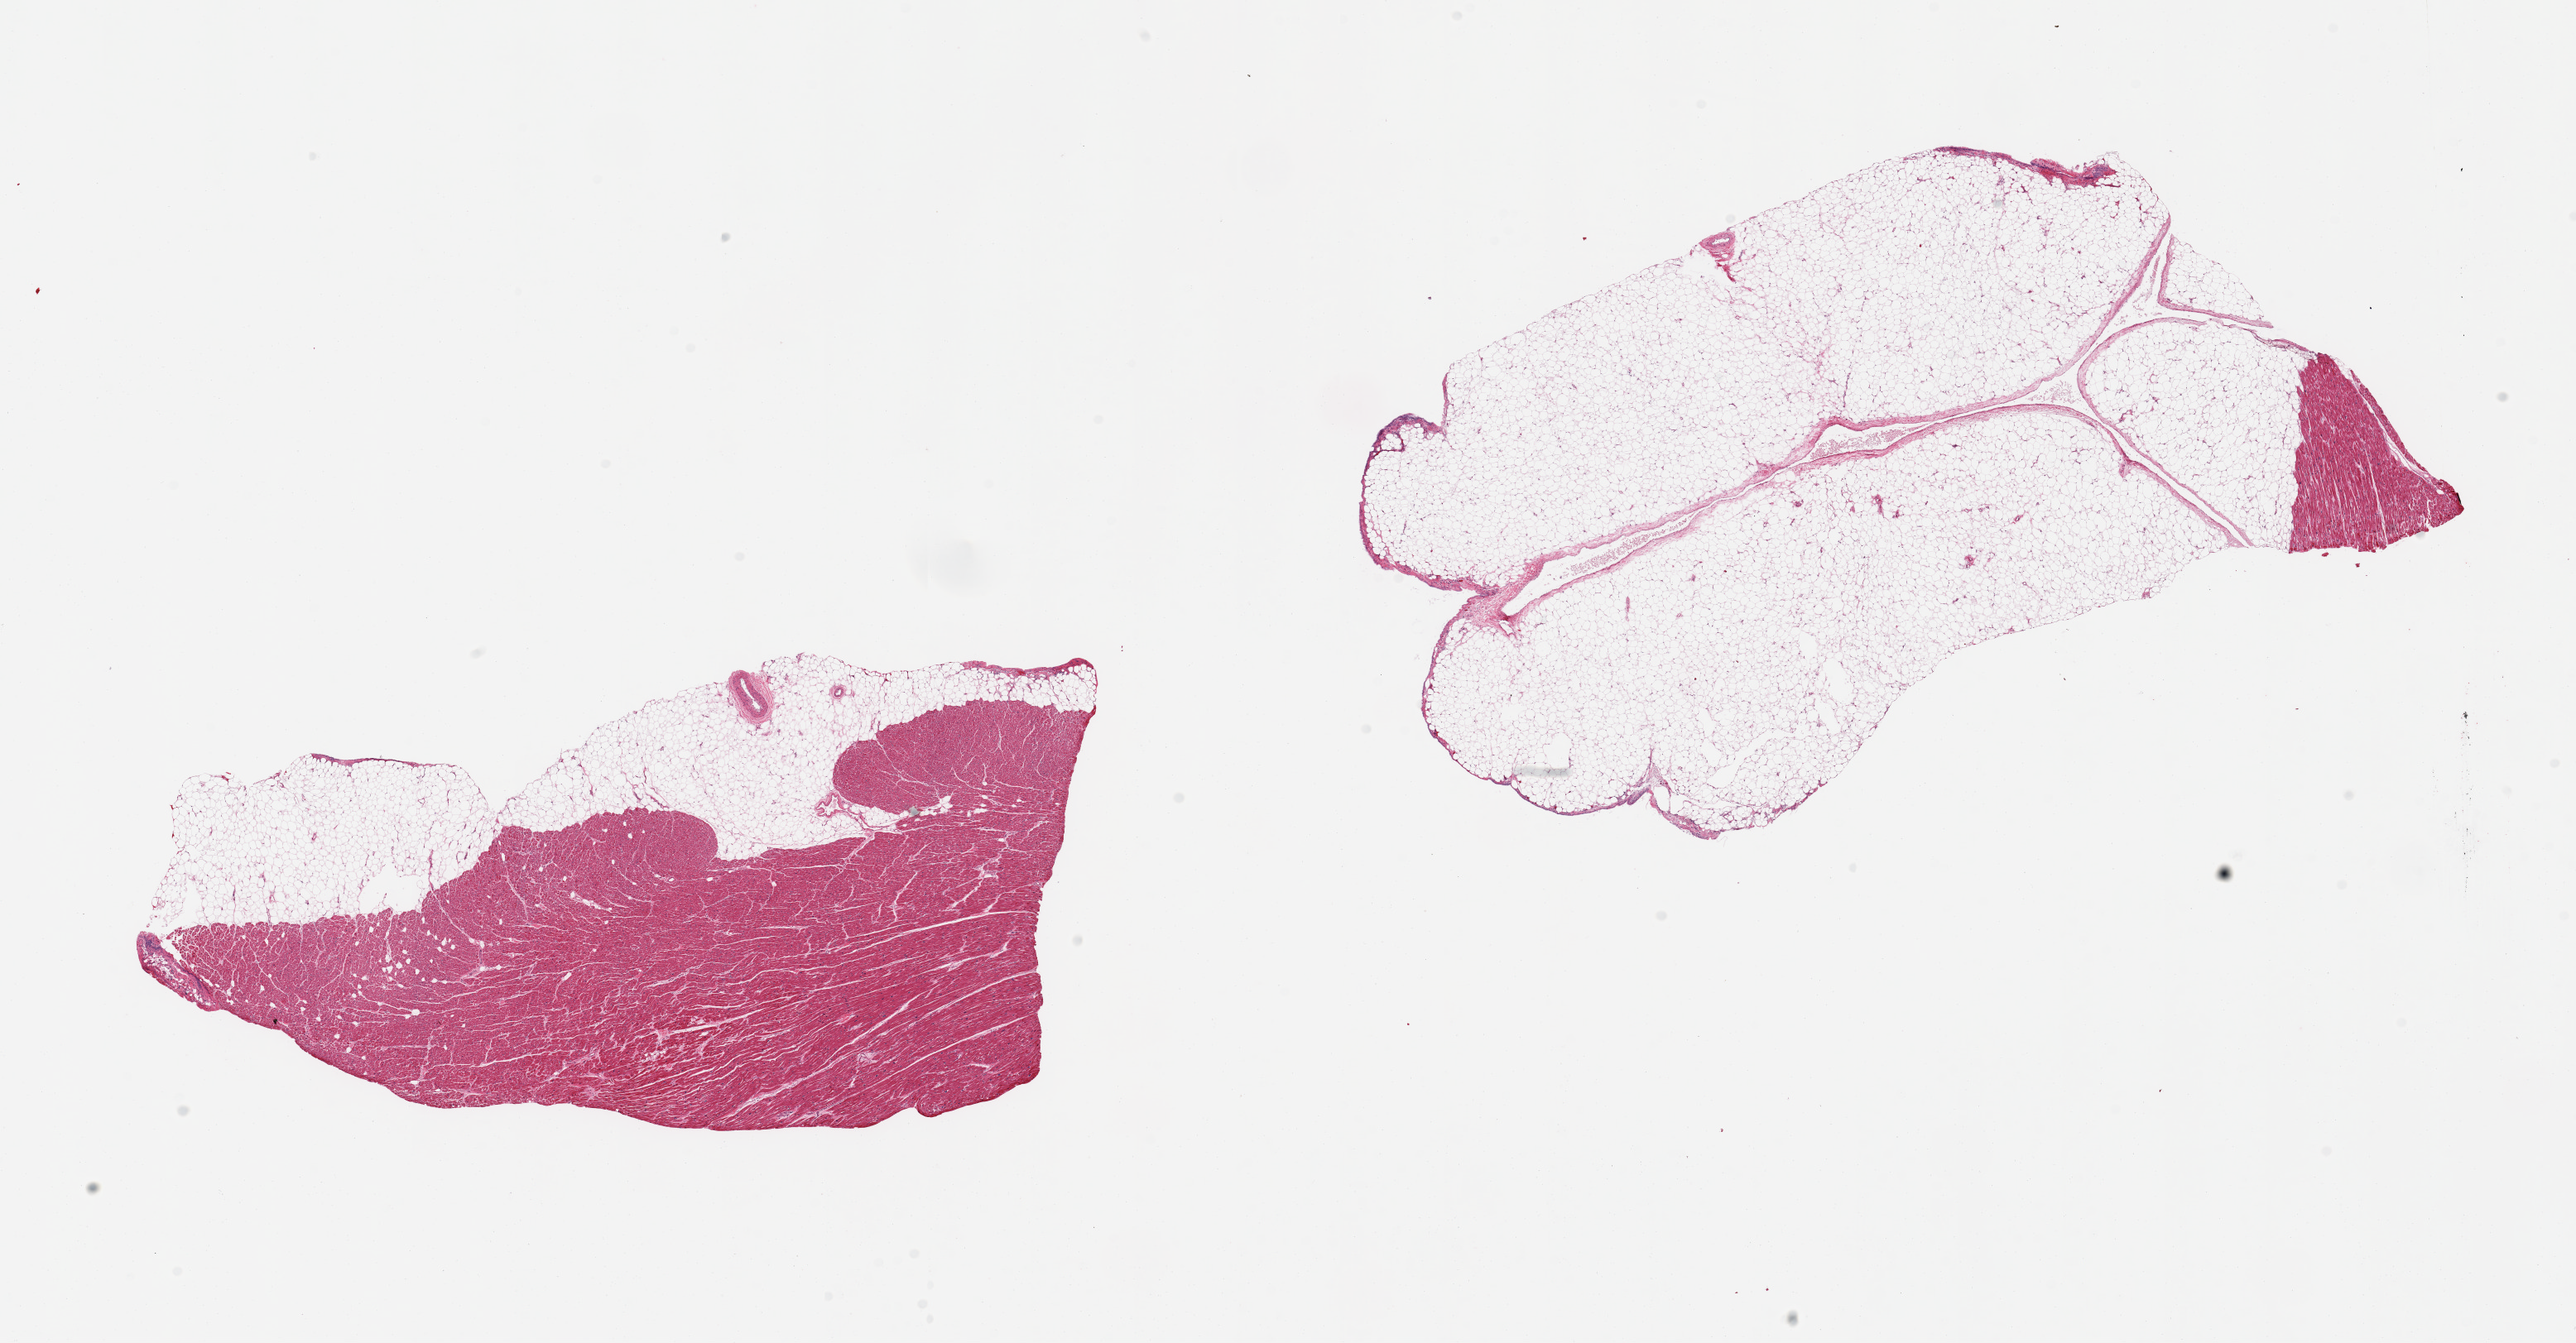
Hematoxylin and eosin (H&E) whole-slide image, brightfield — a low-resolution overview of the entire scanned area, about 24.6 x 12.8 mm (from a 20x scan), PAXgene-fixed, paraffin-embedded tissue, section of heart (target tissue), tissue donor sample. Female donor.
Pathologist's review note for this sample: 2 pieces: 1 is 90% fat, other 30% fat.